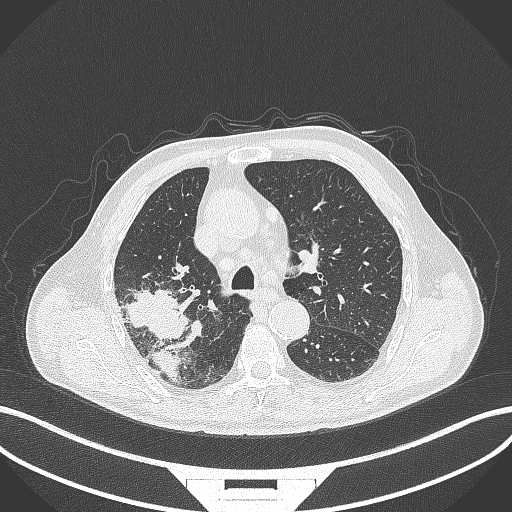
Chest CT, one axial slice. Position 281 of 429 along the scan axis. 120 kVp. Lung window (W 1500 / L -600 HU). 1 mm slice thickness. 512 × 512 image matrix. Patient: male, 72 years. Case-level facts recorded for this patient, not image findings: clinical TNM (as recorded): T3 N2 M0.
Outlined on this slice (rectangle marked by the reading radiologist):
- lung tumour (recorded histology: adenocarcinoma): box from (x=120, y=280) to (x=197, y=393) px